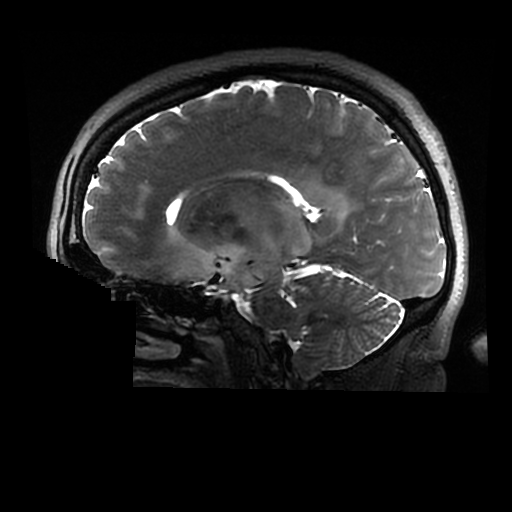
Brain MRI from a brain-tumour surgery series, one sagittal slice. Position 175 of 320 along the scan axis. 0.6 mm slice thickness. 512 × 512 image matrix, field of view 240 × 240 mm. Case-level facts recorded for this patient, not image findings: histopathology: Astrocytoma; WHO grade: 2; IDH mutation: yes.
Structures marked on this image (expert manual segmentation):
- tumour: bounding box <201,198,345,301> (left, top, right, bottom; pixels)